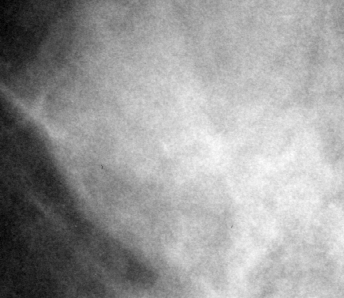
Crop from a digitized film mammogram around one marked abnormality; right breast; MLO view; BI-RADS breast density category 2 (scale 1–4).
Finding: mass, shape oval, margins circumscribed; BI-RADS assessment category 4; pathology result (as recorded, not read from the image): benign.